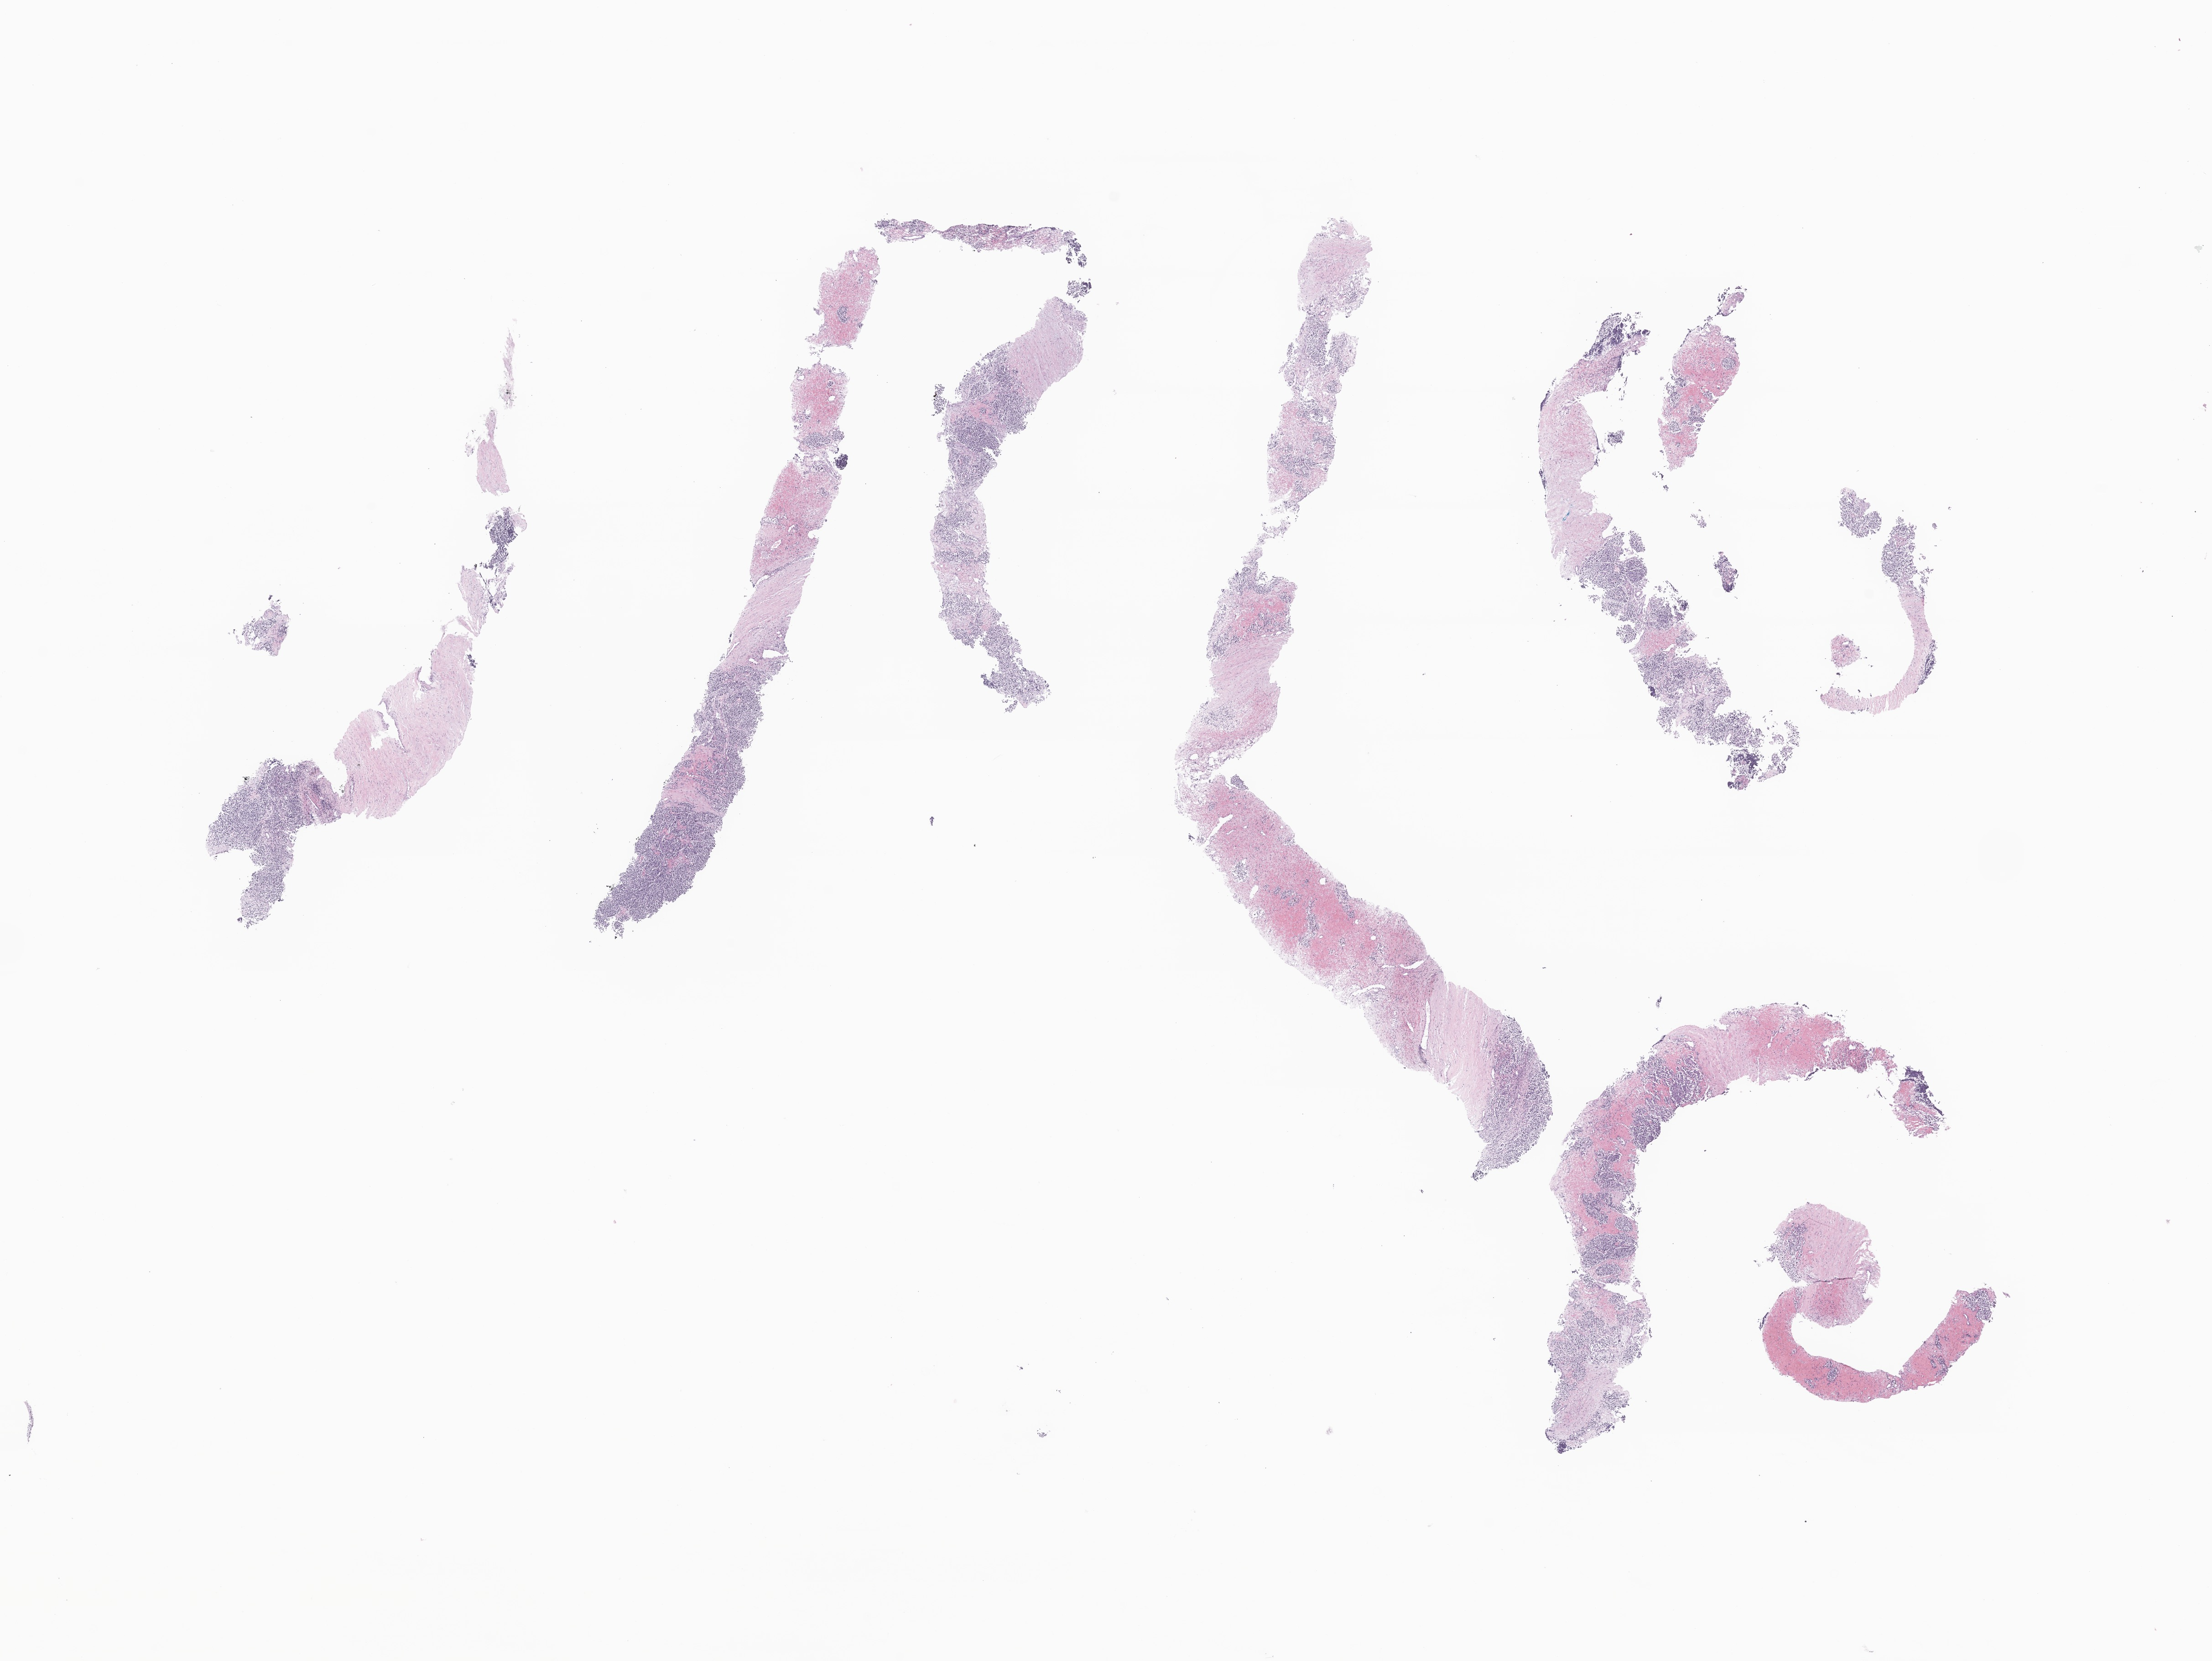
Whole-slide image, haematoxylin and eosin stain of tumor tissue from the adrenal gland, whole scanned area (about 20.4 x 15.3 mm) shown as a low-resolution overview, formalin-fixed, paraffin-embedded (FFPE) tissue. Patient female; age 163 months (13 years 7 months).
Diagnosis: Neuroblastoma, NOS.